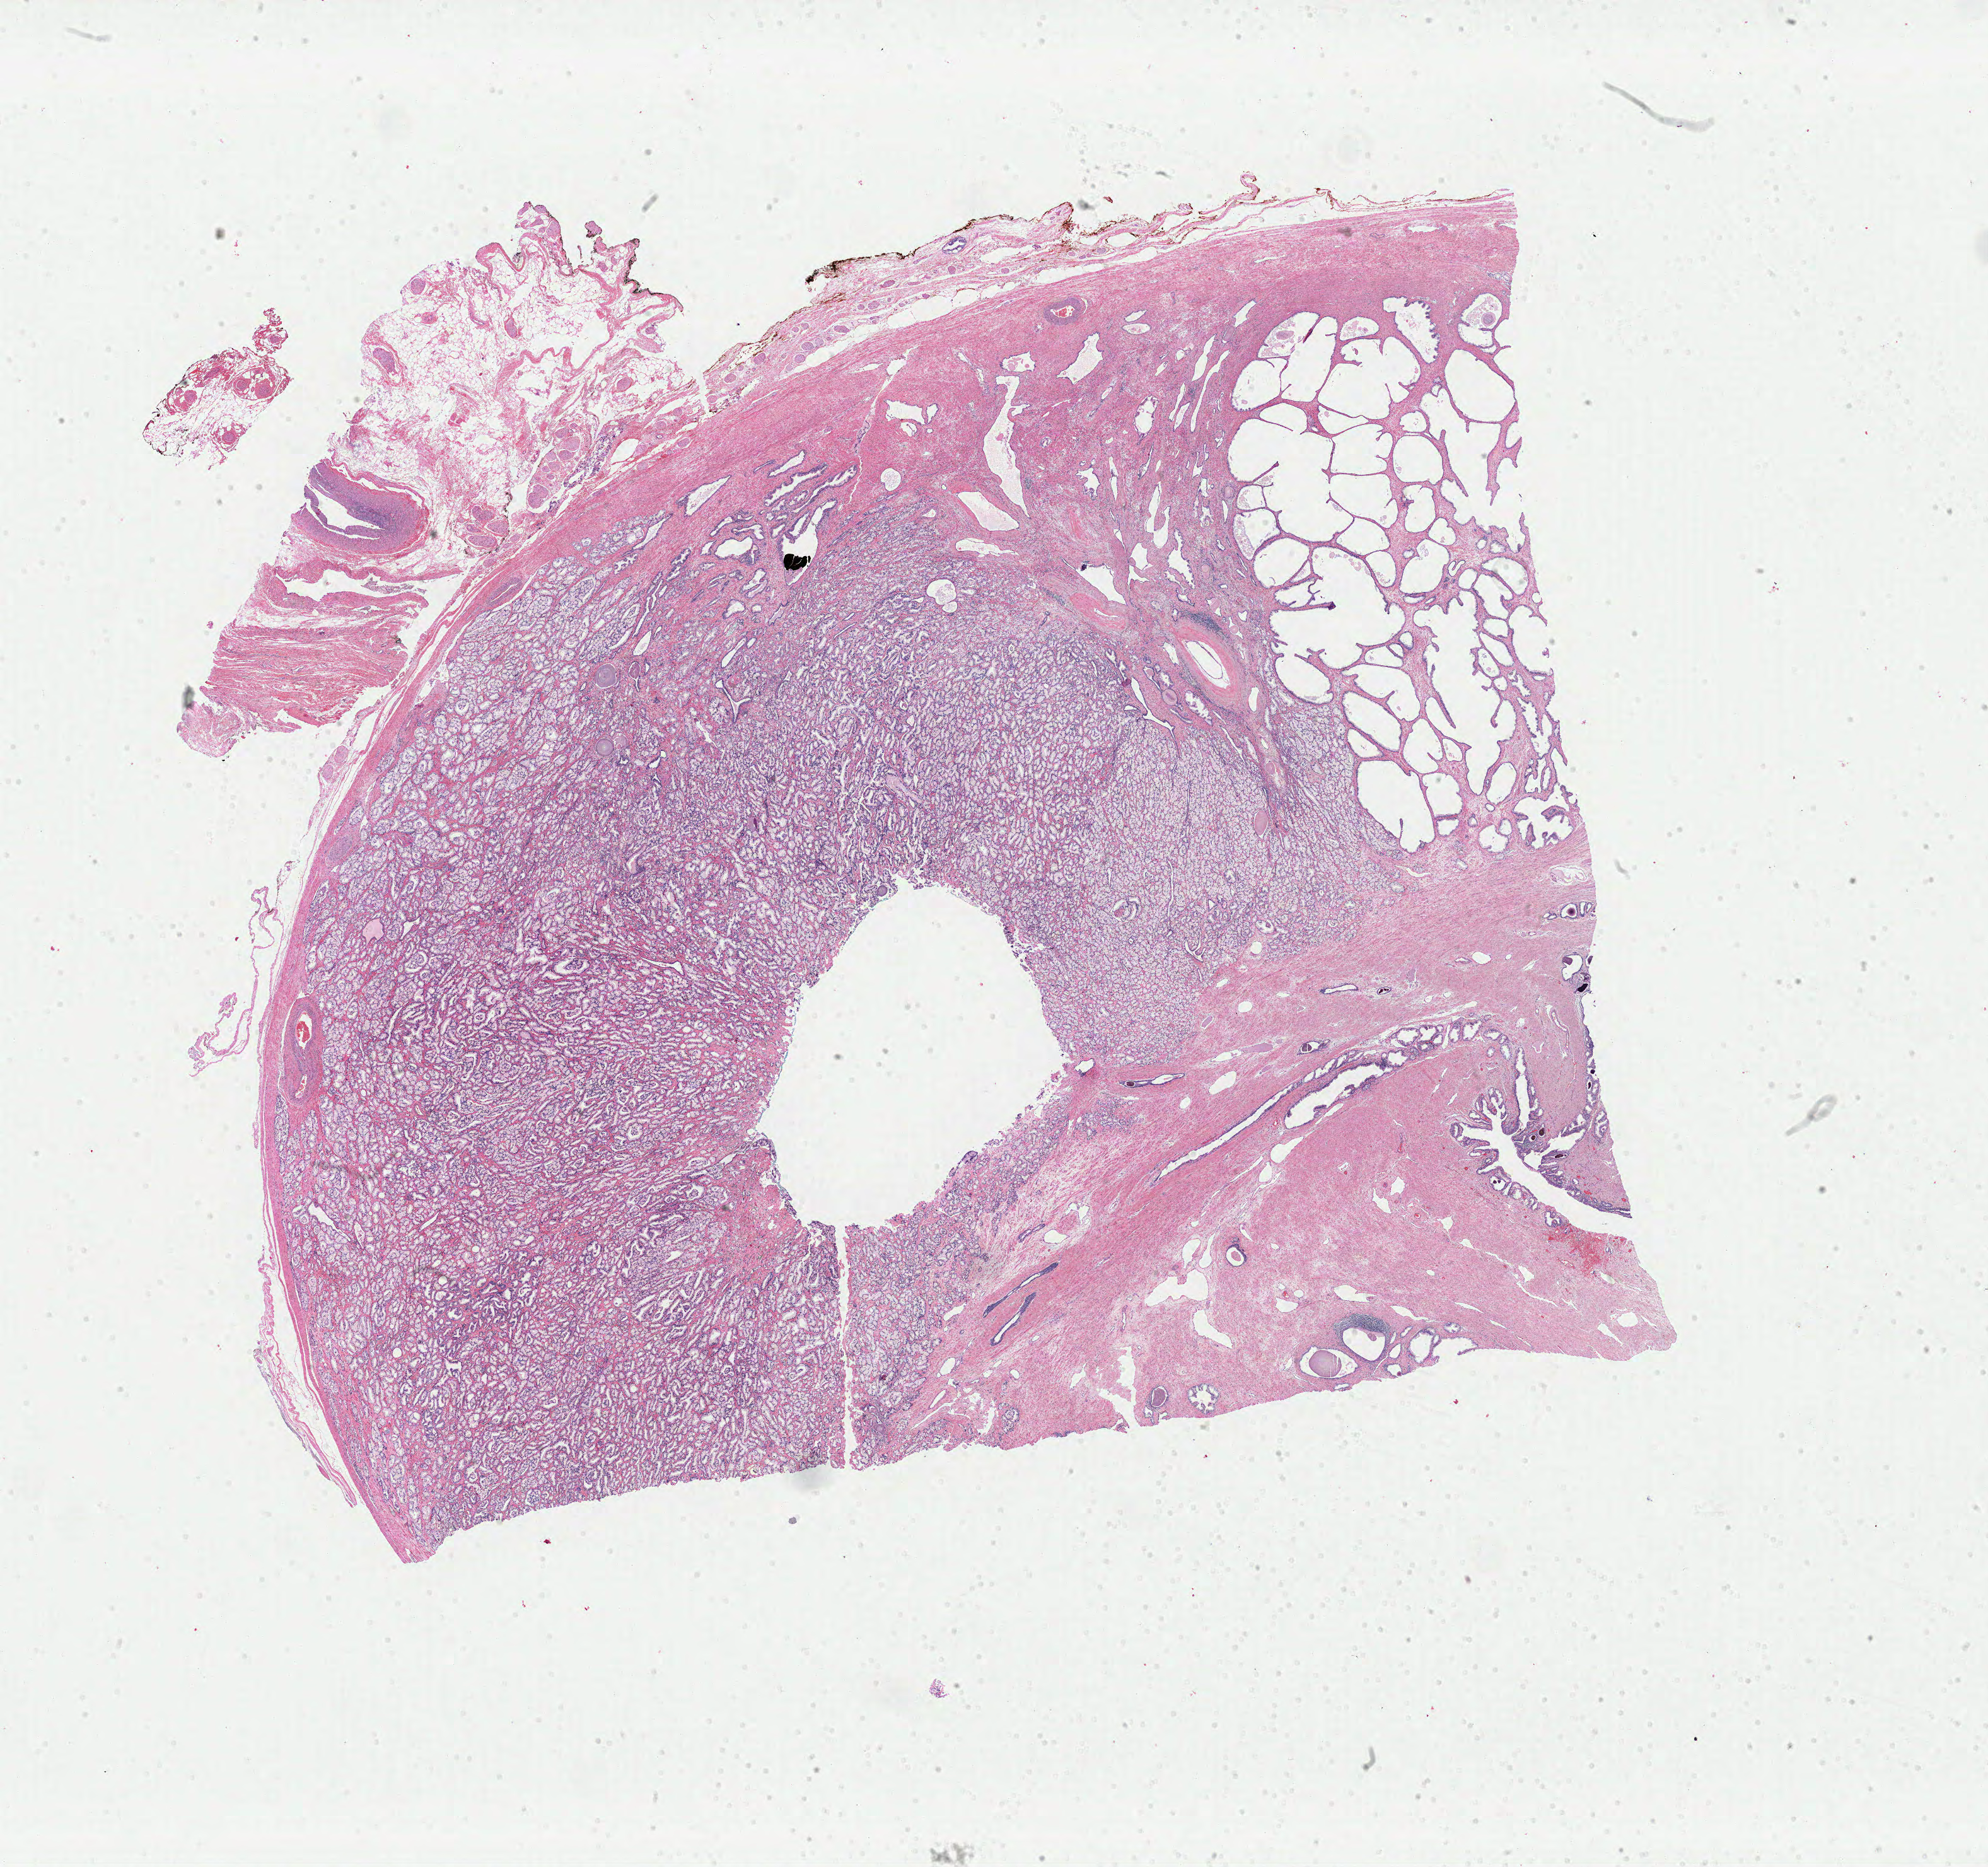
Whole-slide histology image, H&E, a low-resolution overview of the entire scanned area, about 24.9 x 23.4 mm; FFPE section; prostate, primary tumour sample. Male patient; age at initial diagnosis 66 years. Gleason score: 7 (4+3).
- lymph nodes positive (case pathology): 0 of 2 examined
- histologic diagnosis: Adenocarcinoma, NOS (prostate gland)
- laterality: bilateral